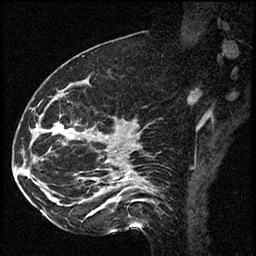
Breast MRI (dynamic contrast-enhanced), one sagittal slice. Position 29 of 60 along the scan axis. Dynamic contrast-enhanced series, image 2 of 2 at this slice position (ordered by acquisition). 1.5 T. TE 4.2 ms, TR 17.3 ms. 2 mm slice thickness. 256 × 256 image matrix, field of view 200 × 200 mm. Female patient. Case-level facts recorded for this patient, not image findings: setting: breast cancer imaged before/during neoadjuvant chemotherapy; receptor status: HR-positive, HER2-negative.
Outlined on this slice (semi-automatically segmented with operator editing):
- analysis volume of interest (the breast-tissue region the enhancement analysis was run in; not a lesion): bounding box (x1, y1, x2, y2) in pixels: (41, 93, 115, 223)
- tumour enhancement mask (voxels above the 100 % enhancement threshold inside the analysis volume of interest): (57, 126, 72, 137)